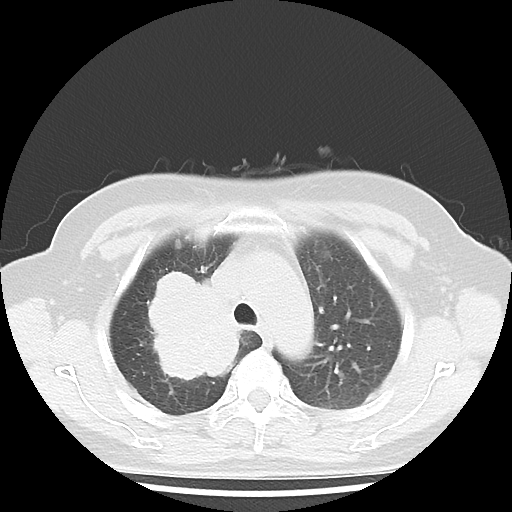
Chest CT, one axial slice; slice 32 of 43 in the series (ordered by position); reconstruction kernel LUNG; lung window (W 1500 / L -600 HU); 512 × 512 image matrix, field of view 316 × 316 mm. Female patient, age 62 years. Case-level facts recorded for this patient, not image findings: clinical TNM (as recorded): T3 N0 M0; histopathological grade: G3.
Structures marked on this image (bounding box drawn by a radiologist):
- lung tumour (recorded histology: small cell carcinoma): bounding box [x1, y1, x2, y2] px = [128, 260, 263, 405]